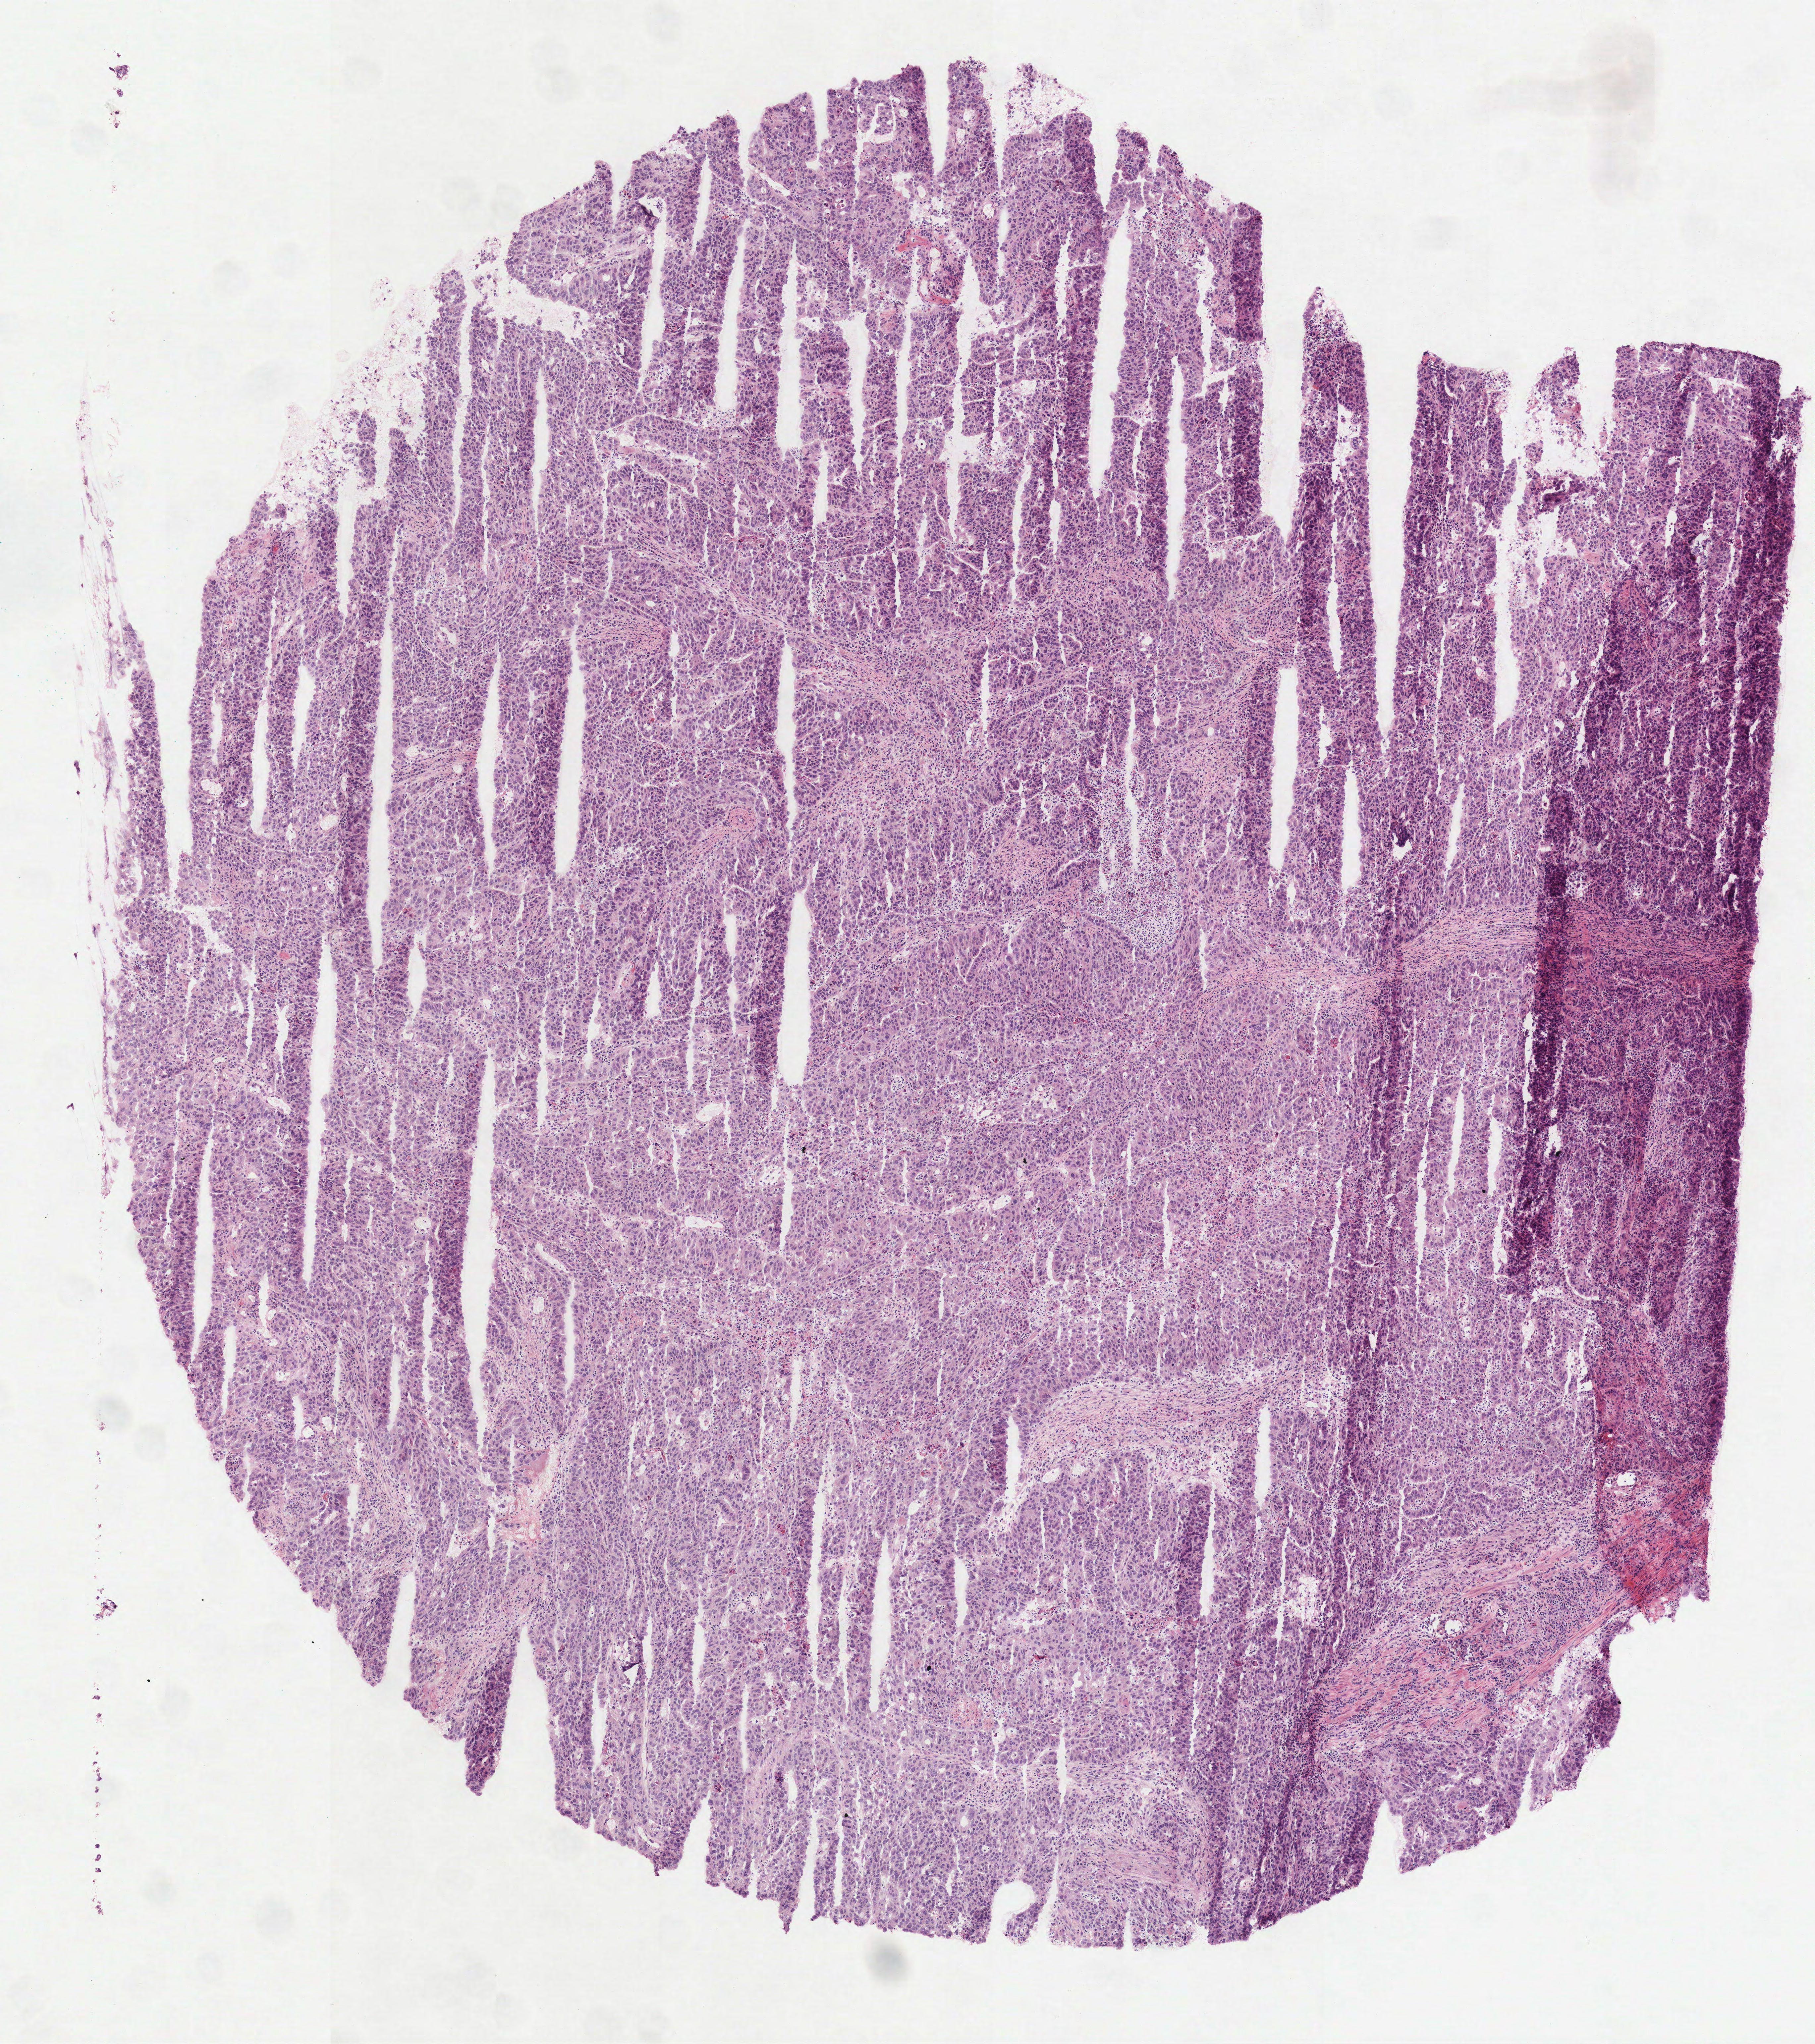
Whole-slide histology image, H&E, a low-resolution overview of the entire scanned area, about 5.5 x 6.2 mm (acquisition: 40x scan), frozen section from the top of the tissue portion, stomach, primary tumour sample. Male patient; age at initial diagnosis 57 years. Histologic grade: G3 (poorly differentiated). Composition of this section per pathologist review: tumour cells 100%, tumour nuclei 80%, normal cells 0%, stromal cells 0%, necrosis 0%. Infiltration values recorded for this section: lymphocyte infiltration 9%, monocyte infiltration 0%, neutrophil infiltration 10%.
* AJCC pathologic stage: IIA (7th edition)
* lymph nodes positive (case pathology): 0 of 20 examined
* pathologic diagnosis: Tubular adenocarcinoma (fundus of stomach)
* TNM: T3 N0 M0